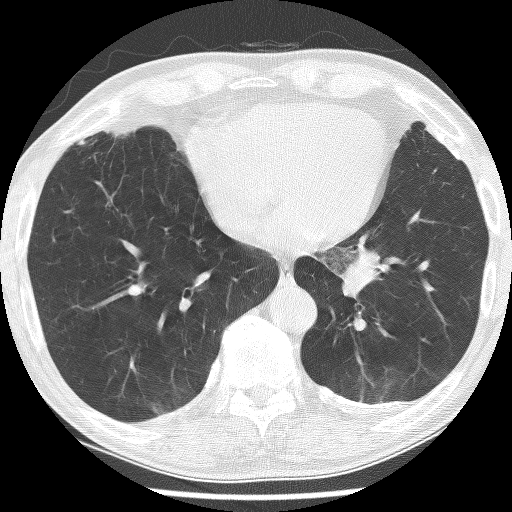
Low-dose screening chest CT, one axial slice. Slice 59 of 226 in the series (ordered by position). Reconstruction kernel BONE. 120 kVp. Lung window (W 1500 / L -600 HU). 512 × 512 image matrix.
Structures marked on this image (expert manual segmentation):
- lesion 1 (tumor, lower lobe of left lung): bounding box (x1, y1, x2, y2) in pixels: (339, 250, 379, 300)